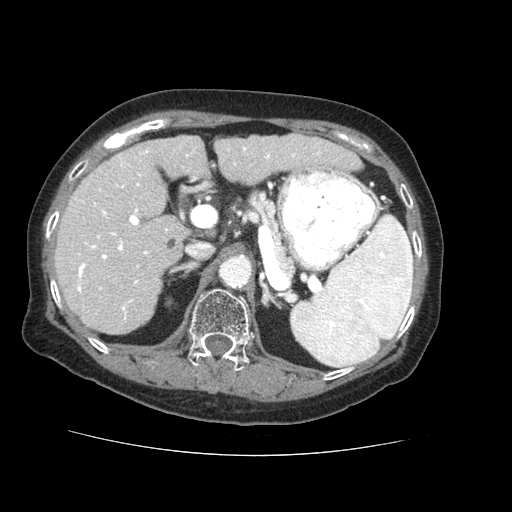
Contrast-enhanced abdominal CT (liver protocol), one axial slice. Slice 34 of 73 in the series (ordered by position). Reconstruction kernel STANDARD. Soft-tissue window (W 400 / L 40 HU). 512 × 512 image matrix, field of view 360 × 360 mm. From the clinical record (not read from this slice): diagnosis: hepatocellular carcinoma (patient treated with transarterial chemoembolisation; whether this scan precedes or follows treatment is not stated here); TNM stage (as recorded): Stage-IVB; Child-Pugh class: A.
Structures marked on this image (semi-automatically segmented with operator editing):
- liver parenchyma outside the tumour (the mass and vessels are separate outlines, so this box may not span the whole liver): bounding box (x1, y1, x2, y2) in pixels: (54, 134, 362, 334)
- liver vessels: (77, 147, 320, 320)